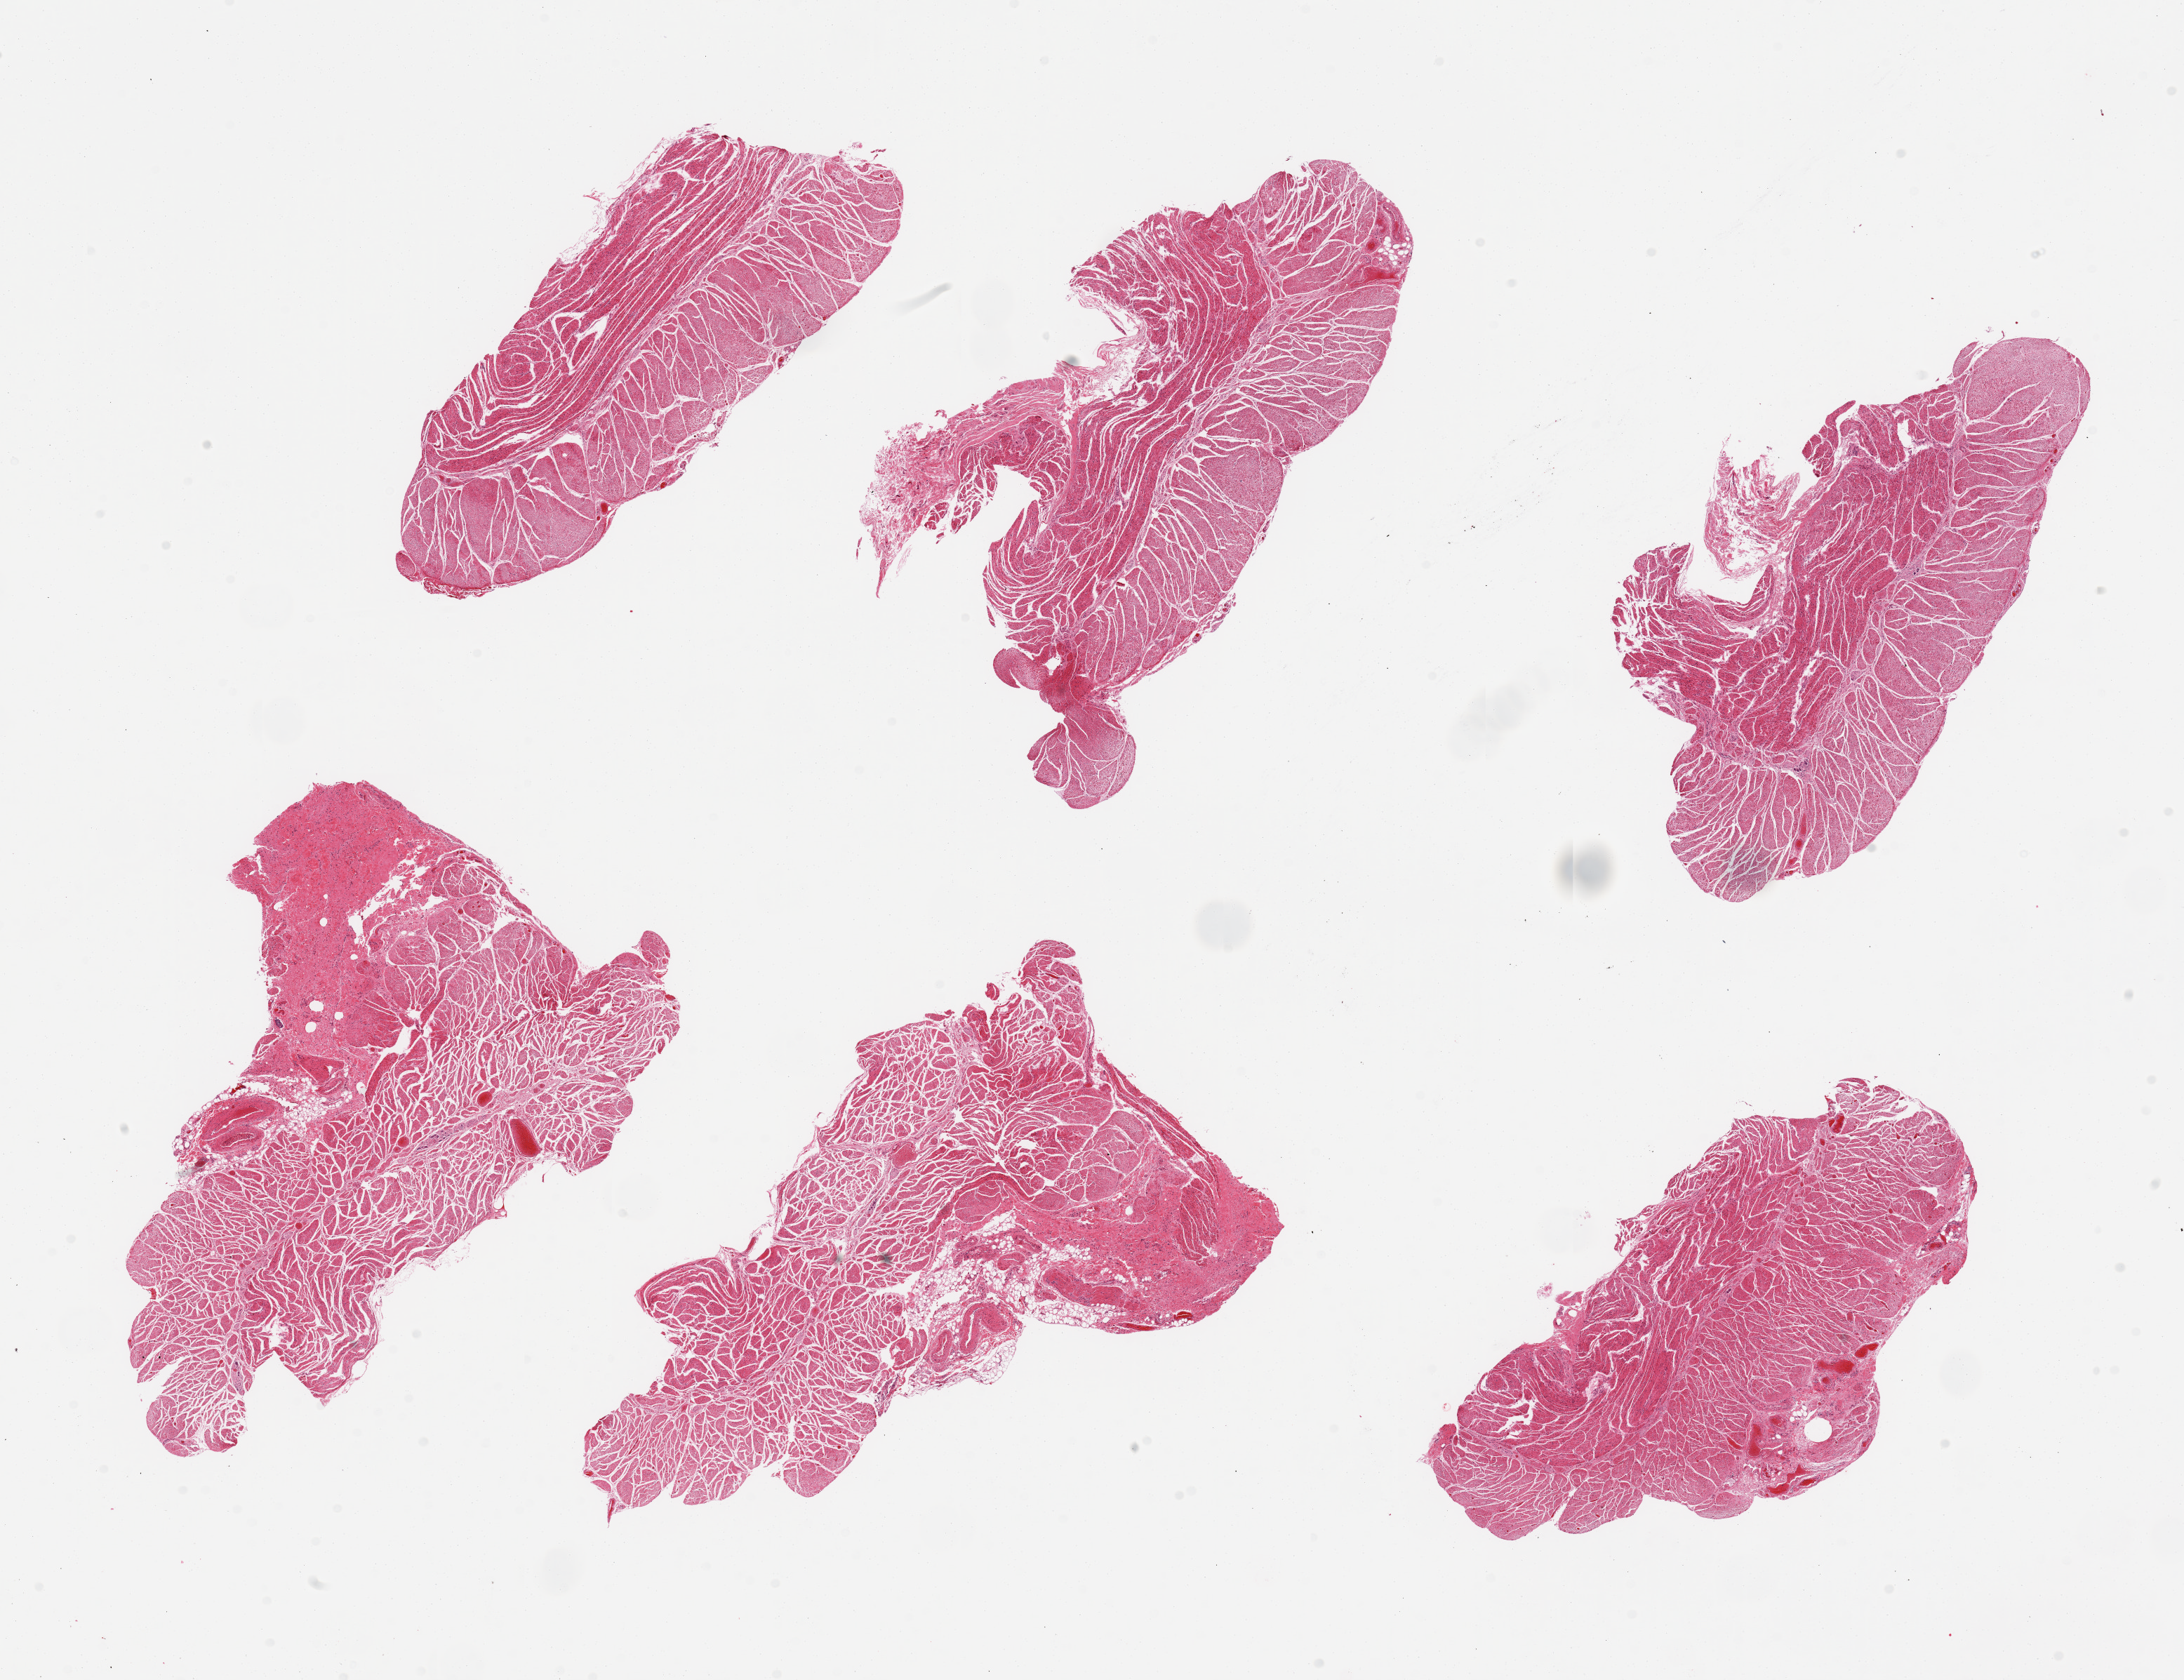
Whole-slide image, haematoxylin and eosin stain — low-resolution overview of the scanned area, about 24.6 x 18.9 mm (from a 20x scan), PAXgene-fixed paraffin-embedded (PFPE) section, sampled site (target tissue): esophageal muscle, donor tissue sample. Donor sex: male.
Reviewer comment on this tissue sample: 6 pieces.